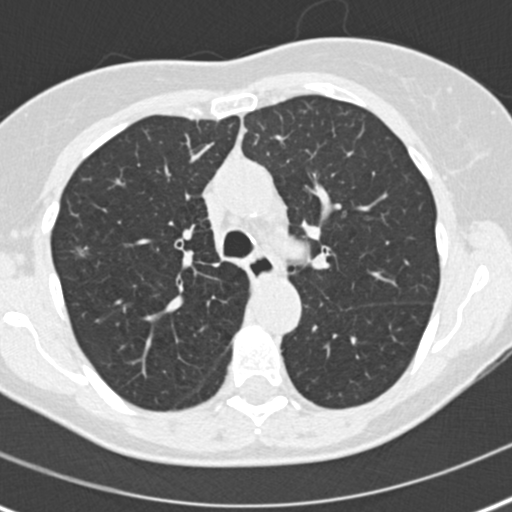
Chest CT (low-dose screening protocol), one axial image; second annual screen; lung window (W 1500 / L -600 HU); 2 mm slice thickness; slice 64 of 186 in the series; 512 × 512 image matrix, field of view 290 × 290 mm. Female, age 60 years at enrolment. Current smoker at enrolment.
• Expert reader's lesion annotation, bounding box (x1, y1, x2, y2) in pixels: (60, 231, 102, 272).
• Reader record for this screening exam (exam-level; its link to the box is not recorded): non-calcified nodule or mass ≥4 mm, right upper lobe, 8 × 6 mm, spiculated (stellate) margins, soft tissue attenuation, pre-existing on the prior screen: no.
• Participant outcome: lung cancer diagnosed 511 days after this screen (after the third annual screen) — bronchiolo-alveolar adenocarcinoma, NOS, right upper lobe, well differentiated (G1), stage IA (AJCC 6th edition), 11 mm at pathology.